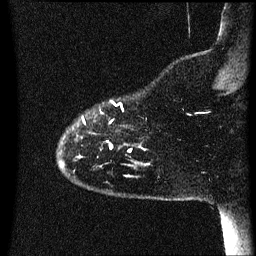
Breast MRI (dynamic contrast-enhanced), one sagittal slice; position 8 of 60 along the scan axis; dynamic contrast-enhanced series, image 2 of 3 at this slice position (ordered by acquisition); 1.5 T; TE 4.2 ms, TR 8.4 ms; 2.2 mm slice thickness; 256 × 256 image matrix. Patient: female, 35 years. Case-level facts recorded for this patient, not image findings: setting: breast cancer imaged before/during neoadjuvant chemotherapy; receptor status: HER2-positive.
Structures marked on this image (semi-automatically segmented with operator editing):
- analysis volume of interest (the breast-tissue region the enhancement analysis was run in; not a lesion): box from (x=59, y=100) to (x=151, y=173) px
- tumour enhancement mask (voxels above the 70 % enhancement threshold inside the analysis volume of interest): (x=110, y=144)–(x=132, y=151)